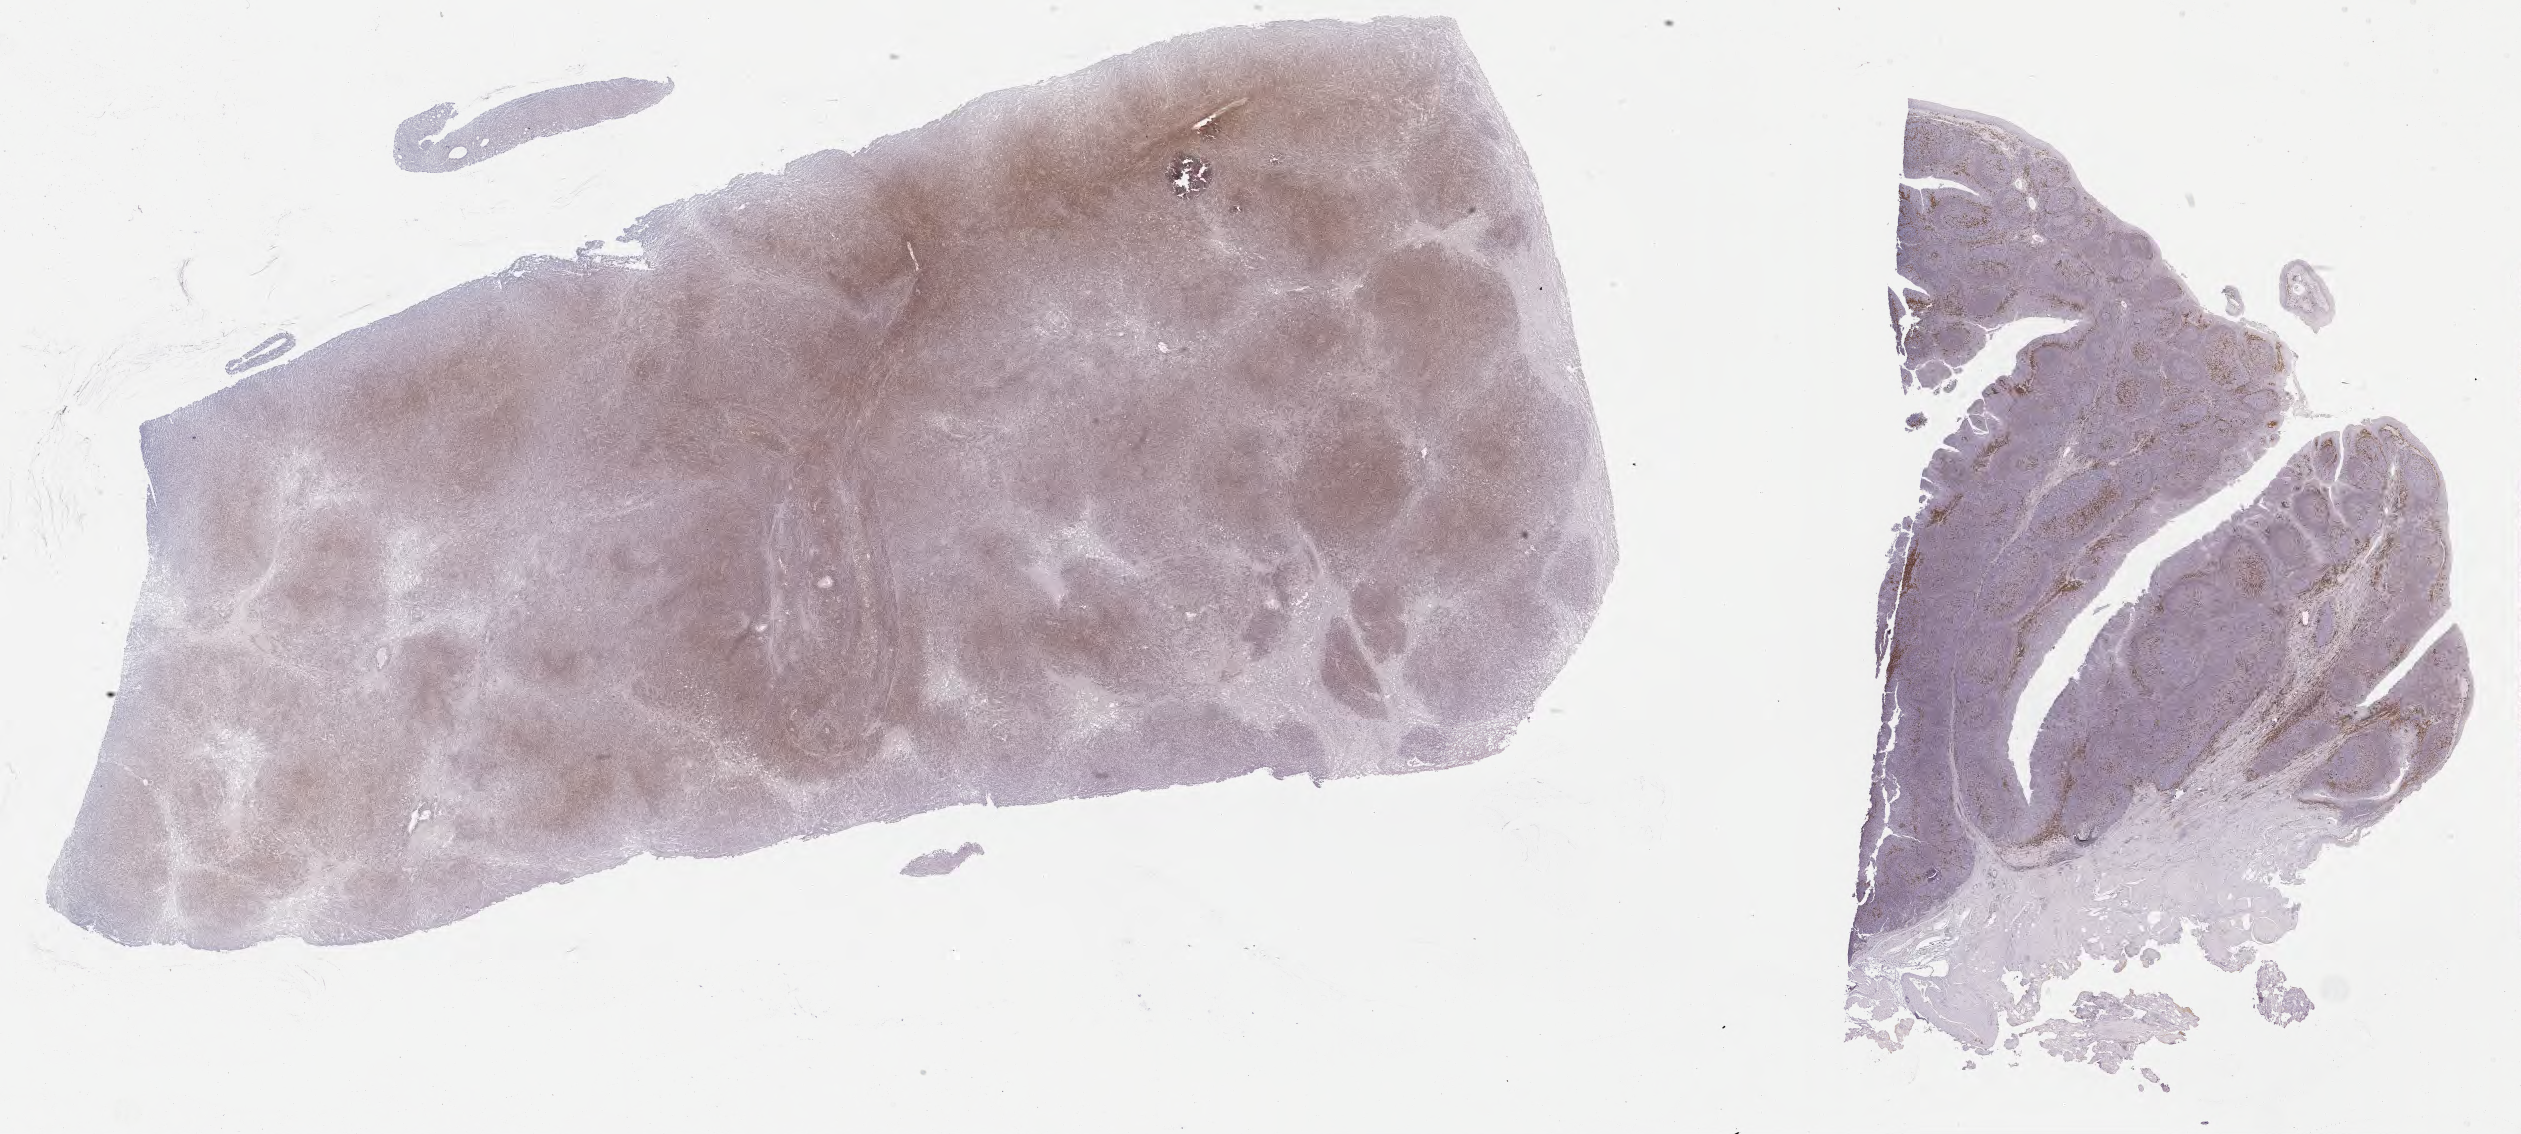
Whole-slide image, immunohistochemical stain for IRF4/MUM1, low-resolution overview of the scanned area, about 40.8 x 18.3 mm. Specimen: tumor tissue. Patient male; age 39 years.
• histologic diagnosis: Diffuse large B-cell lymphoma, NOS